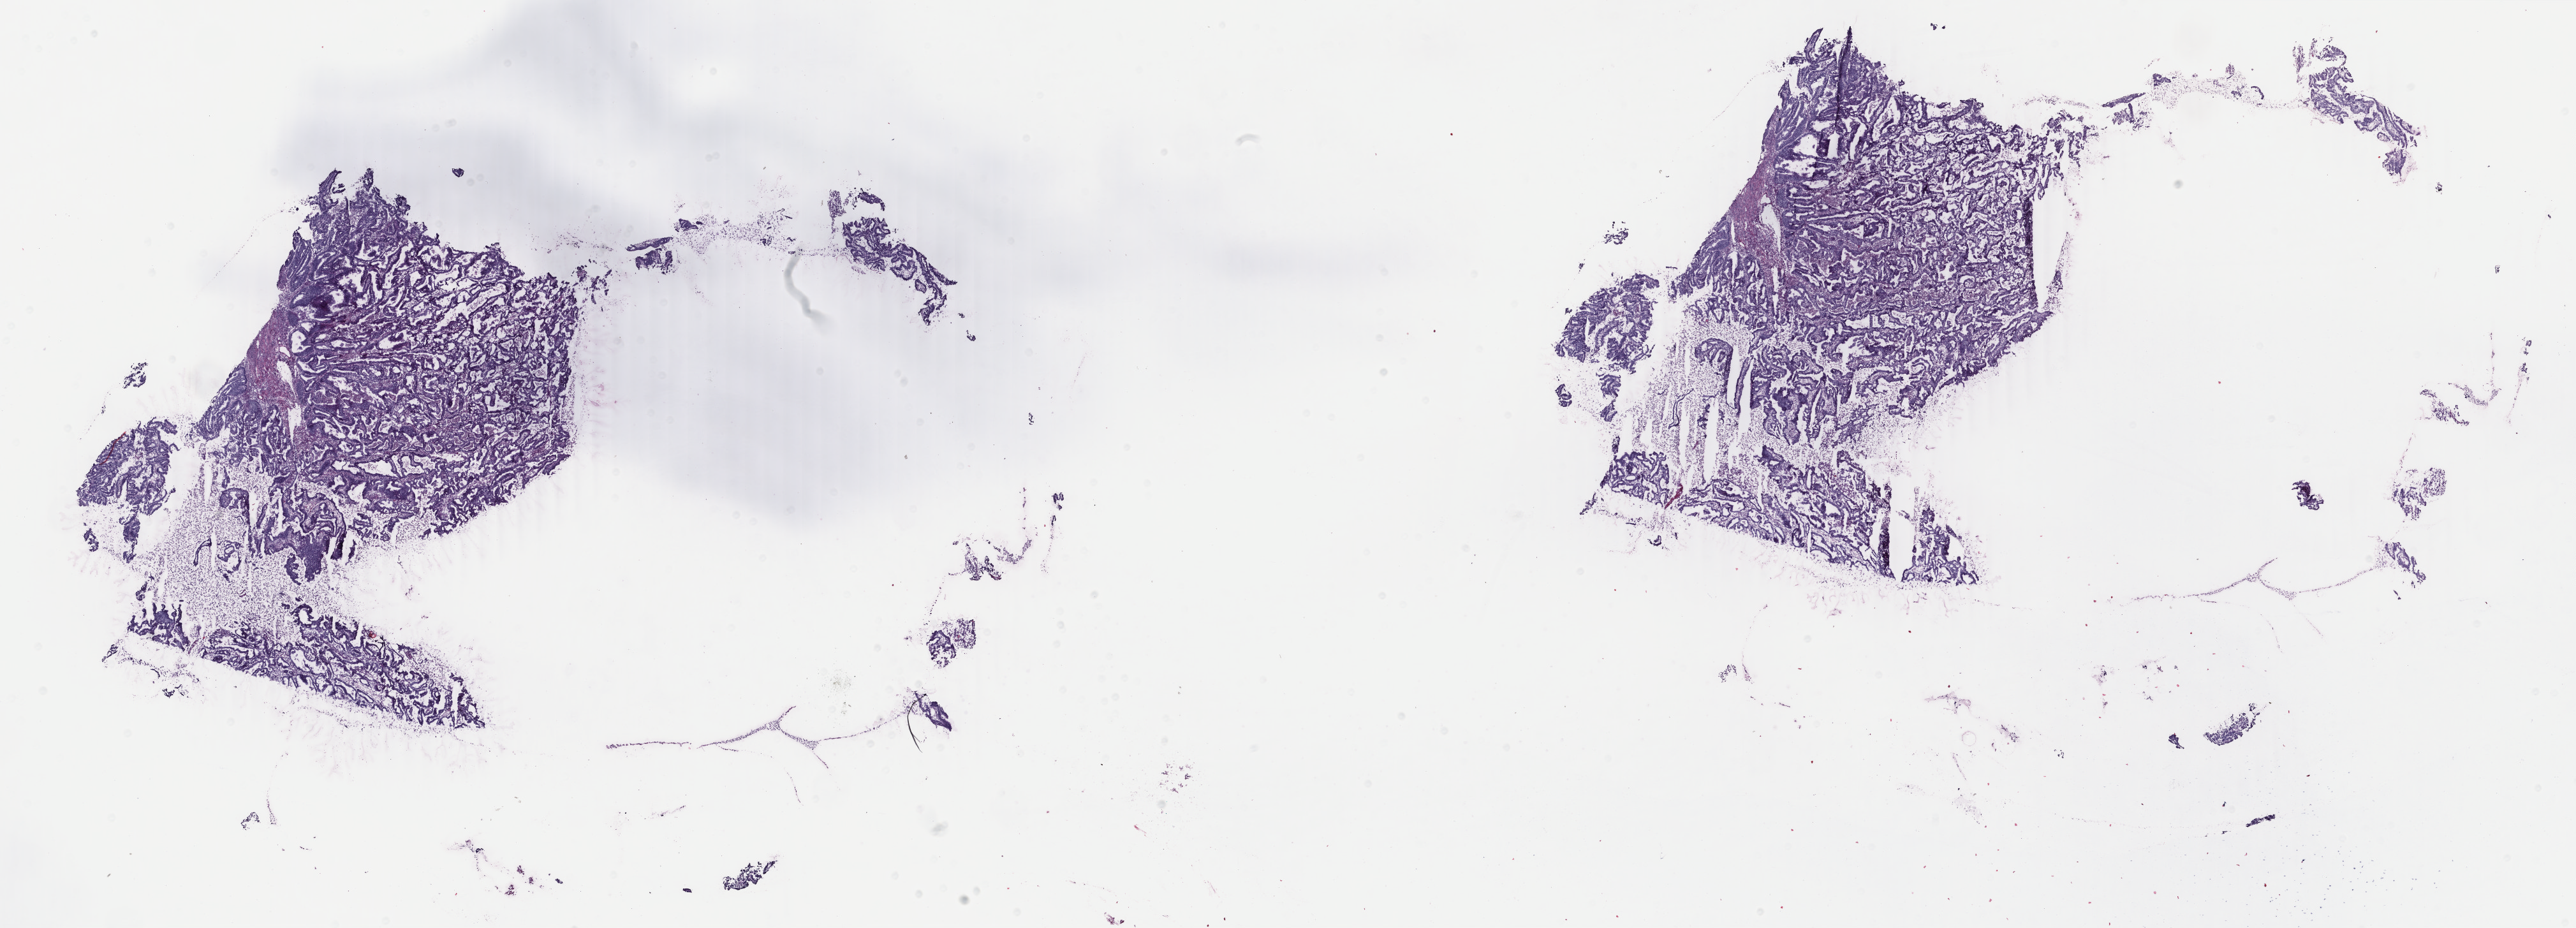
Digitized H&E tissue section (whole slide), a low-resolution overview of the entire scanned area, about 32.1 x 11.6 mm; frozen section; primary tumour sample from the uterus. Patient: female, age at initial diagnosis 73 years. Histologic grade: G1 (well differentiated). Pathologist review of this section (percent, as recorded): tumour cells 77%, tumour nuclei 65%, normal cells 10%, stromal cells 10%, necrosis 3%. Inflammatory infiltration, as recorded: lymphocyte infiltration 1%, monocyte infiltration 1%, neutrophil infiltration 20%.
Pathologic diagnosis: Endometrioid adenocarcinoma, NOS. FIGO stage: IA.